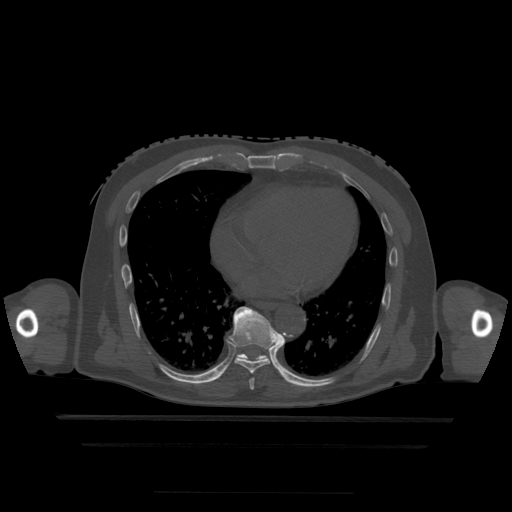
CT including the spine, one axial slice. Bone window (W 1800 / L 400 HU). 1.25 mm slice thickness. 512 × 512 image matrix. Patient age 68 years. From the clinical record (not read from this slice): primary cancer: urothelial.
Structures marked on this image (semi-automatically segmented with operator editing):
- T7 vertebra: bounding box [x1, y1, x2, y2] px = [249, 379, 255, 390]
- T8 vertebra: [229, 307, 279, 374]
- T9 vertebra: [236, 354, 268, 361]